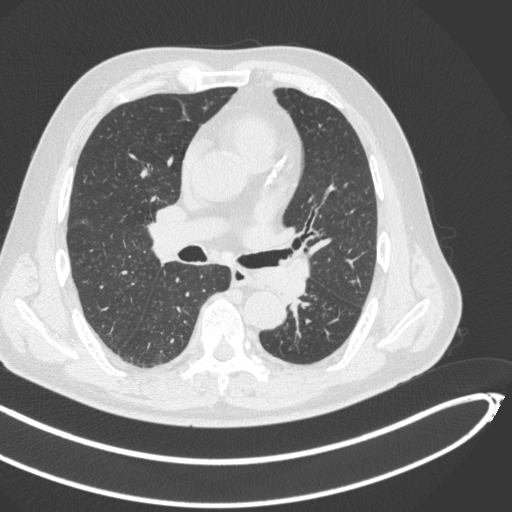
Chest CT, one axial slice; reconstruction kernel B31f; 120 kVp; lung window (W 1500 / L -600 HU); 1 mm slice thickness; 512 × 512 image matrix. Patient: male, 64 years. Case-level facts recorded for this patient, not image findings: clinical TNM (as recorded): T1c N0 M0; histopathological grade: G2.
Annotated regions visible in this slice (bounding box drawn by a radiologist):
- lung tumour (recorded histology: squamous cell carcinoma): box from (x=252, y=261) to (x=309, y=301) px